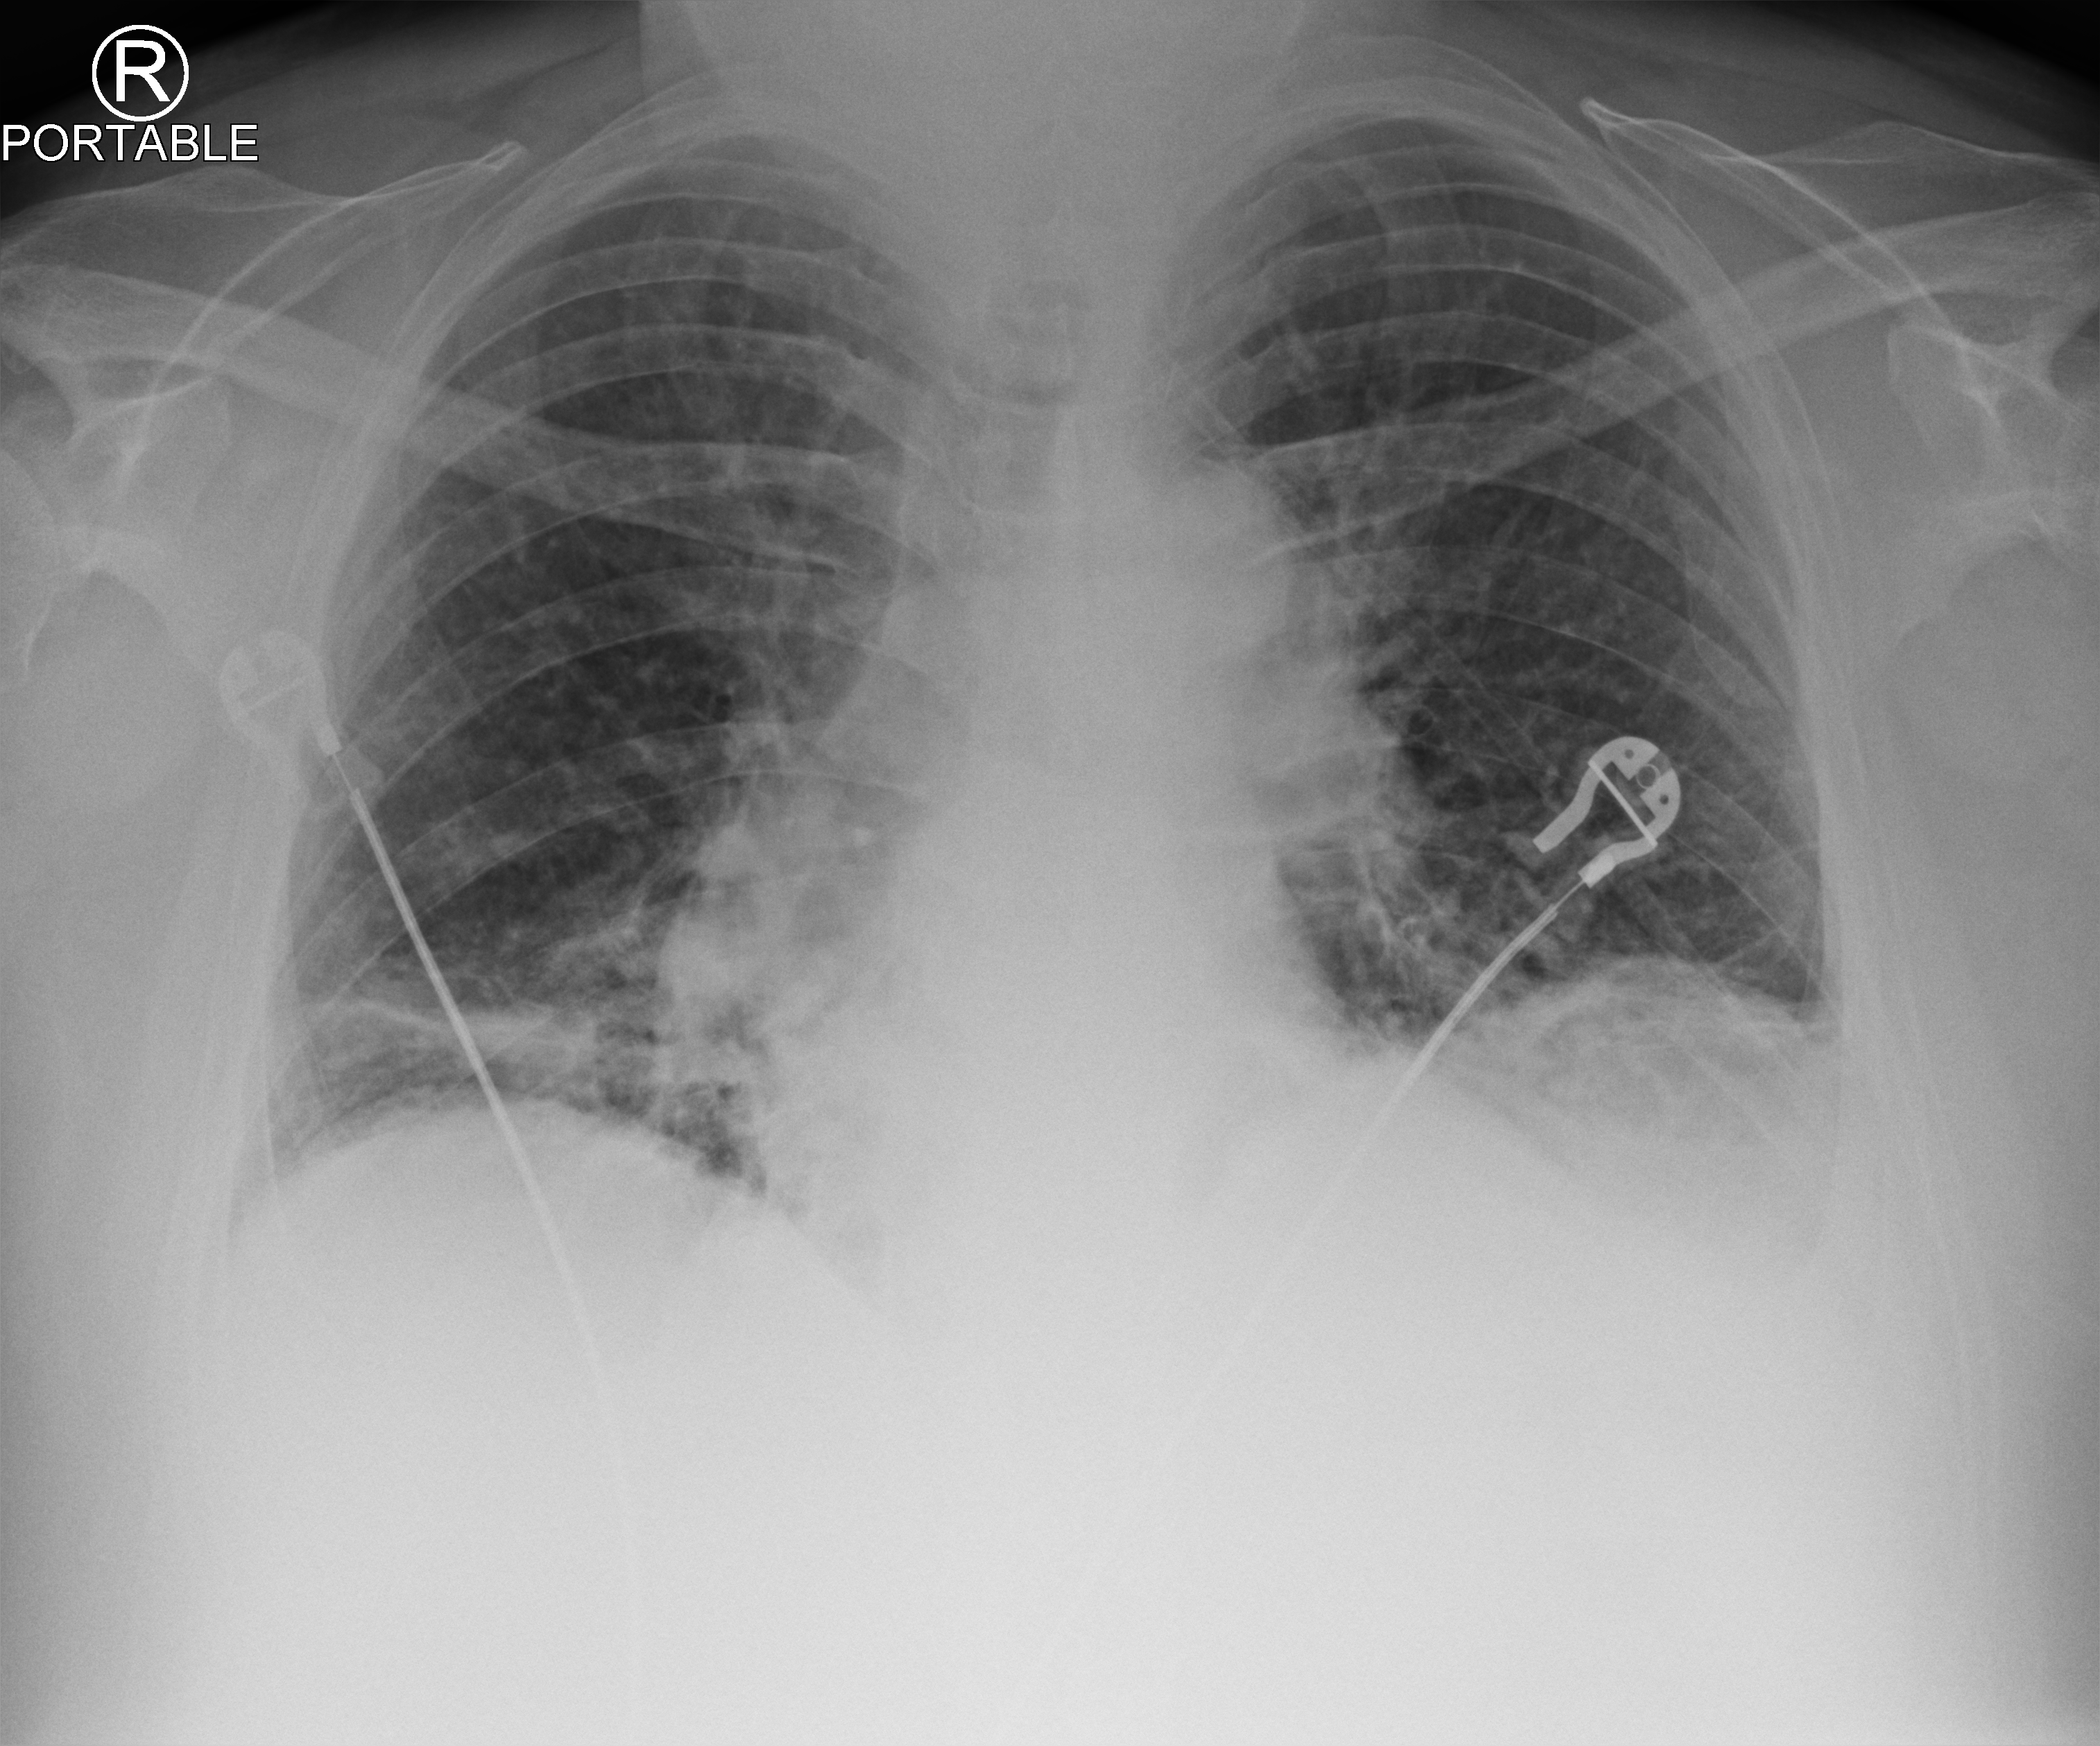
Chest X-ray (portable); anteroposterior (AP) projection. Patient hospitalised with COVID-19; male, aged 60–74 years.
From the hospital-stay record, not from the radiograph (when in the stay this image was taken is not recorded): hypertension (admission record): no; admitted to intensive care during this hospital stay: yes; smoking status (admission record): never.